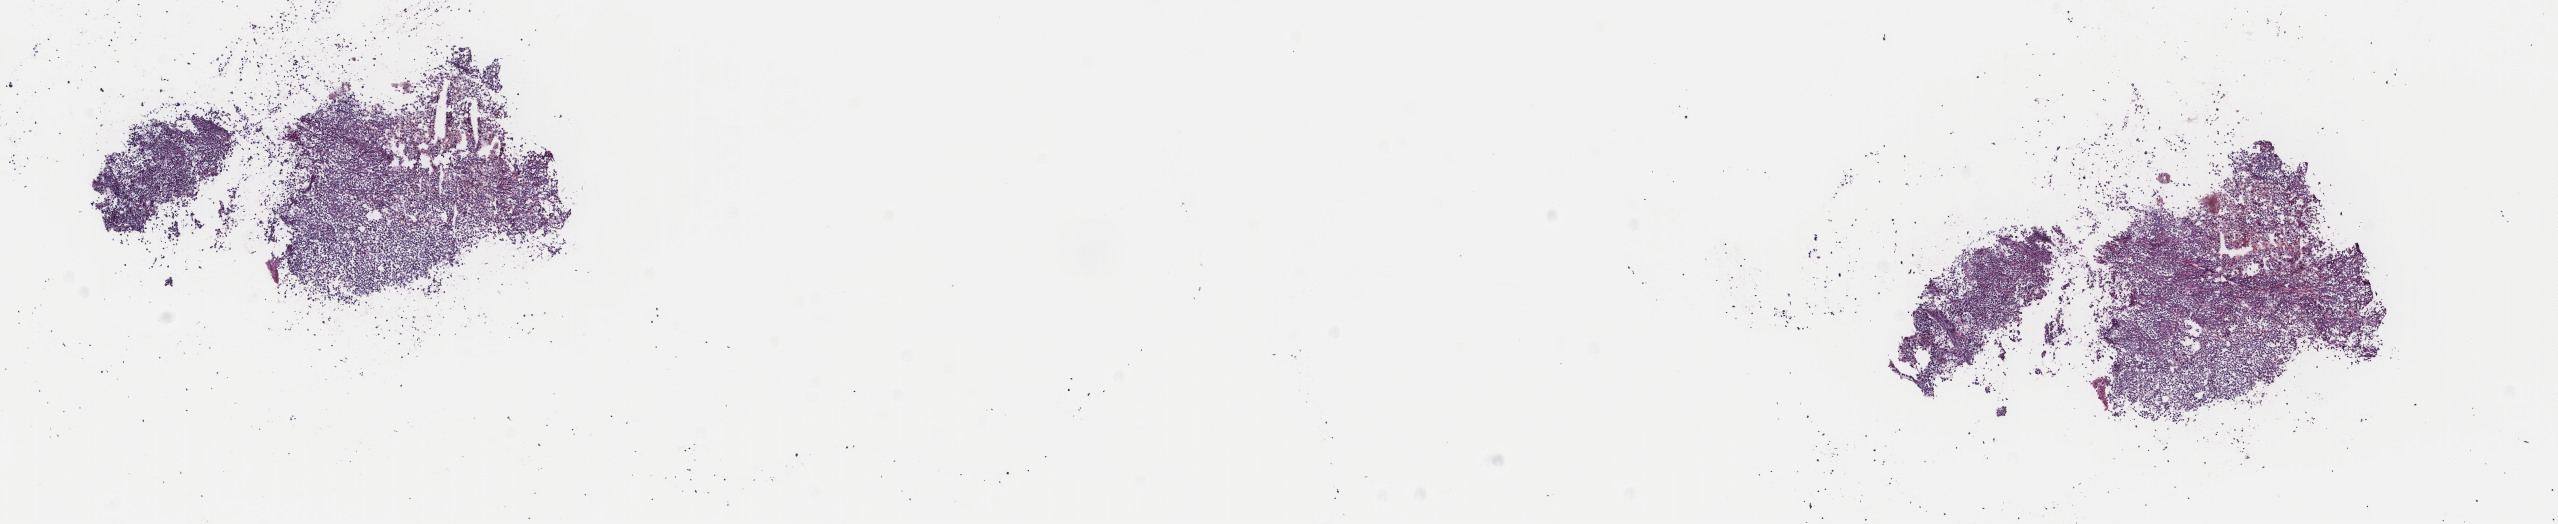
Digitized H&E tissue section (whole slide) — a low-resolution overview of the entire scanned area, about 20.3 x 4.2 mm (slide scanned at 40x); frozen section from the top of the tissue portion; metastatic tumour sample, sampled site: lymph nodes of inguinal region or leg. Patient: male, age at initial diagnosis 44 years. Composition of this section per pathologist review: tumour cells 96%, tumour nuclei 98%, normal cells 0%, stromal cells 0%, necrosis 4%. Inflammatory infiltration, as recorded: lymphocyte infiltration 0%, monocyte infiltration 0%, neutrophil infiltration 0%.
* this section: metastatic tumour tissue
* patient diagnosis: Malignant melanoma, NOS